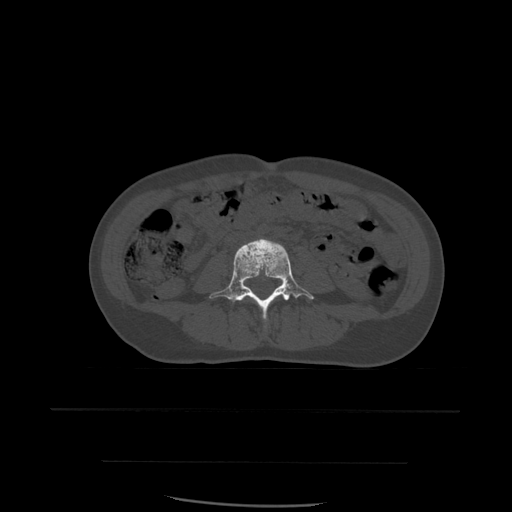
CT including the spine, one axial slice. Position 175 of 574 along the scan axis. Bone window (W 1800 / L 400 HU). 1.25 mm slice thickness. 512 × 512 image matrix, field of view 392 × 392 mm. Patient age 48 years. Case-level facts recorded for this patient, not image findings: primary cancer: lung; vertebrae with lytic lesions (as recorded): T11.
Structures marked on this image (semi-automatic segmentation, software-assisted and operator-edited):
- L4 vertebra: bounding box (x1, y1, x2, y2) in pixels: (210, 239, 314, 320)